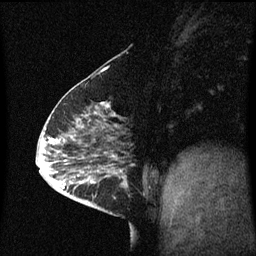
Breast MRI (dynamic contrast-enhanced), one sagittal slice; slice 22 of 60 in the series (ordered by position); dynamic contrast-enhanced series, image 2 of 3 at this slice position (ordered by acquisition); 1.5 T; TE 4.2 ms, TR 8.4 ms; 256 × 256 image matrix. Female patient, age 63 years.
Structures marked on this image (semi-automatically segmented with operator editing):
- analysis volume of interest (the breast-tissue region the enhancement analysis was run in; not a lesion): bounding box <98,168,145,217> (left, top, right, bottom; pixels)
- tumour enhancement mask (voxels above the 70 % enhancement threshold inside the analysis volume of interest): <98,170,127,185>